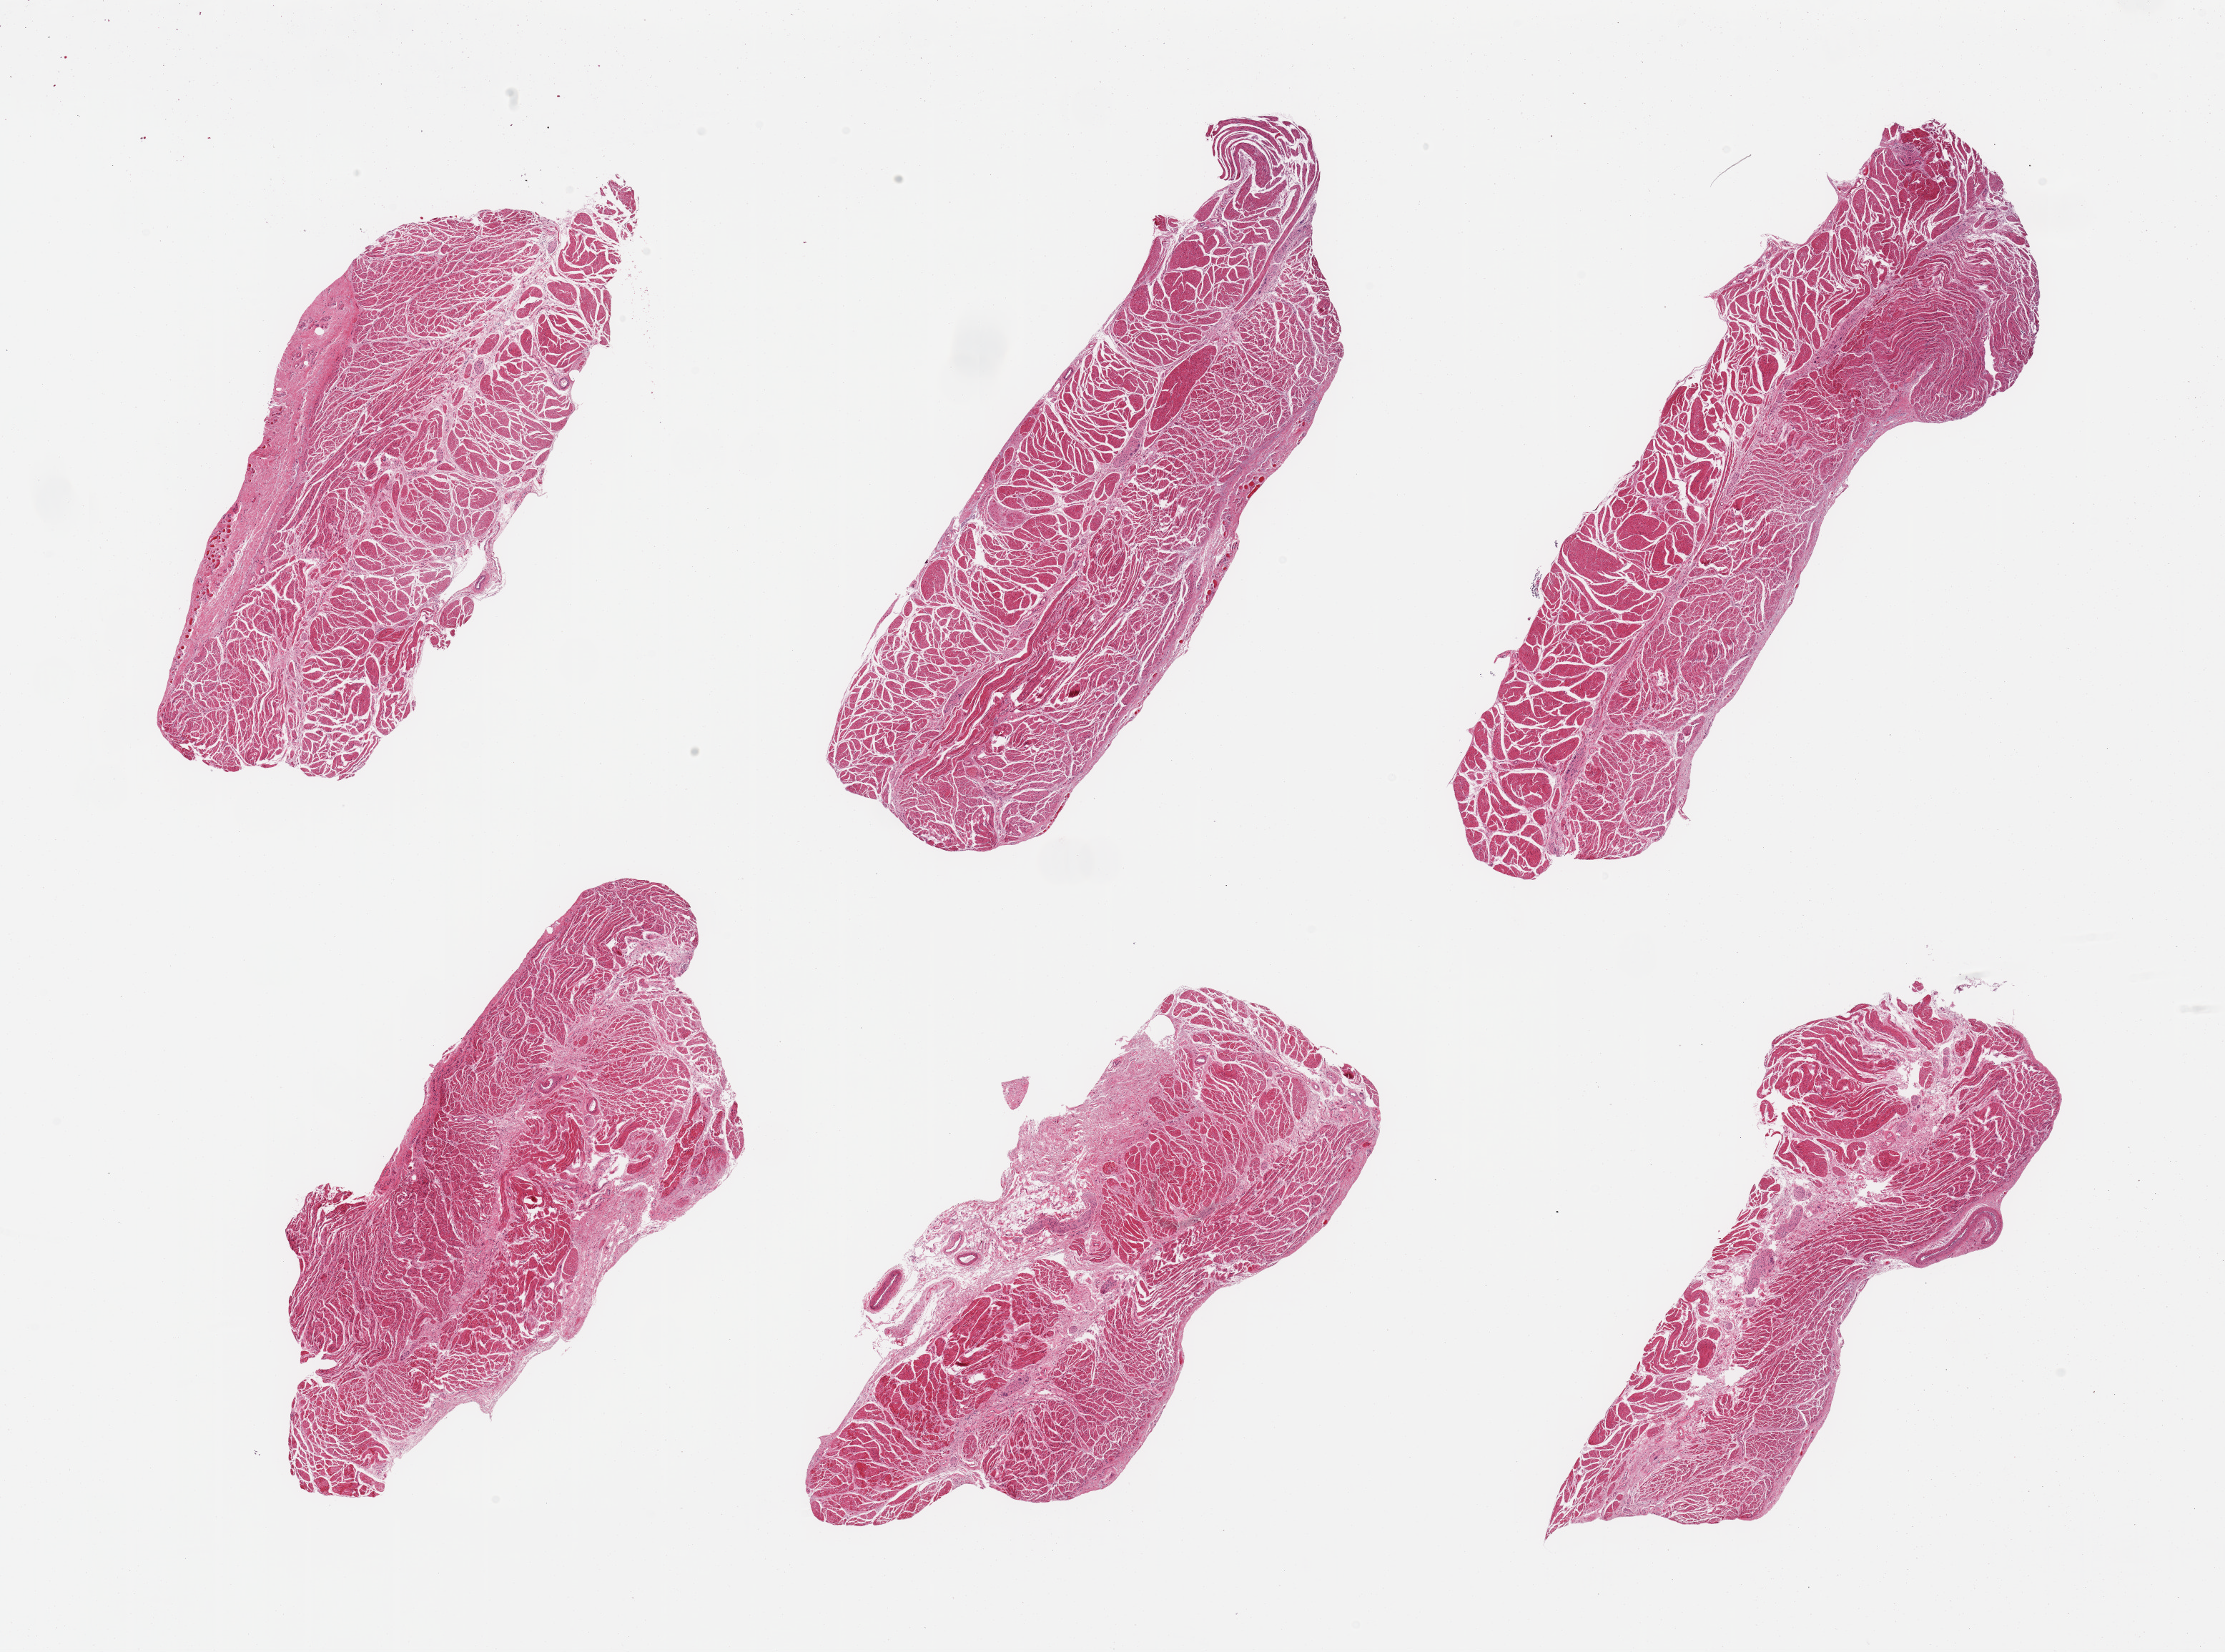
Hematoxylin and eosin (H&E) whole-slide image, shown as a low-resolution overview of the whole scanned area (about 24.6 x 18.3 mm); PAXgene-fixed, paraffin-embedded tissue; section of gastroesophageal junction (target tissue); donor tissue sample. Male donor.
Review note (as recorded): 6 pieces; essentially well trimmed target muscularis; trace rim of serosa on one section.